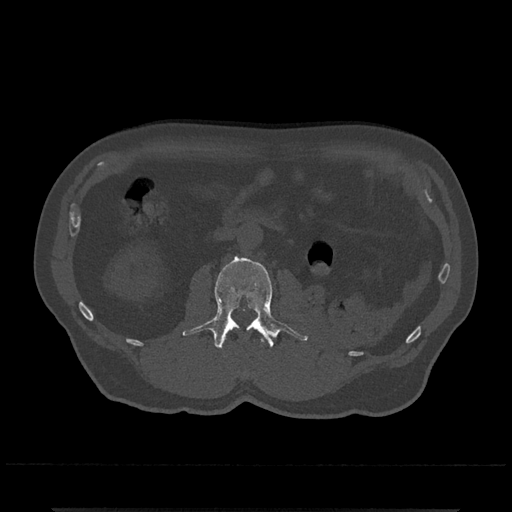
CT including the spine, one axial slice. Slice 299 of 797 in the series (ordered by position). 120 kVp. Bone window (W 1800 / L 400 HU). 0.5 mm slice thickness. 512 × 512 image matrix, field of view 393 × 393 mm. Patient: male, 67 years. Case-level facts recorded for this patient, not image findings: primary cancer: prostate.
Outlined on this slice (semi-automatic segmentation, software-assisted and operator-edited):
- L1 vertebra: bounding box [x1, y1, x2, y2] px = [261, 339, 265, 344]
- L2 vertebra: [182, 256, 308, 349]